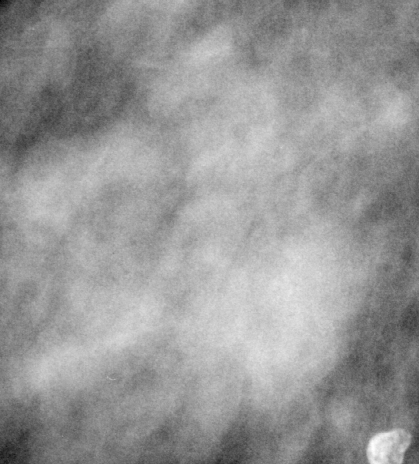
Cropped region of a digitized screen-film mammogram centred on a radiologist-marked abnormality, right breast, MLO view, BI-RADS breast density category 2 (scale 1–4).
Finding: mass, shape lobulated, margins microlobulated; BI-RADS assessment category 3; subtlety rating 5 on a 1 (subtle) to 5 (obvious) scale; benign; no additional work-up was recommended (benign without callback).